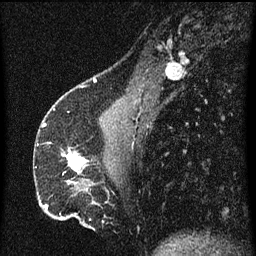
Breast MRI (dynamic contrast-enhanced), one sagittal slice. Position 21 of 60 along the scan axis. Dynamic contrast-enhanced series, image 2 of 3 at this slice position (ordered by acquisition). 1.5 T. TE 4.2 ms, TR 8 ms. 2 mm slice thickness. 256 × 256 image matrix, field of view 180 × 180 mm. Female patient, age 51 years.
Annotated regions visible in this slice (semi-automatic segmentation, software-assisted and operator-edited):
- analysis volume of interest (the breast-tissue region the enhancement analysis was run in; not a lesion): box from (x=68, y=150) to (x=89, y=175) px
- tumour enhancement mask (voxels above the 70 % enhancement threshold inside the analysis volume of interest): (x=68, y=150)–(x=85, y=171)